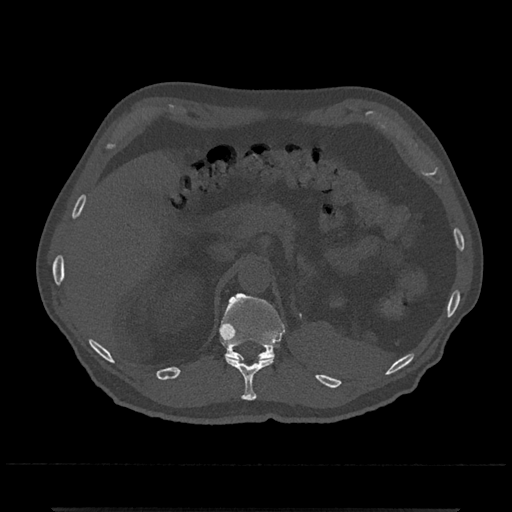
CT including the spine, one axial slice. Slice 459 of 797 in the series (ordered by position). Reconstruction kernel Br40s/3. 120 kVp. Bone window (W 1800 / L 400 HU). 0.5 mm slice thickness. 512 × 512 image matrix. Patient: male, 67 years. From the clinical record (not read from this slice): primary cancer: prostate.
Outlined on this slice (semi-automatic segmentation, software-assisted and operator-edited):
- T11 vertebra: bounding box (x1, y1, x2, y2) in pixels: (225, 356, 274, 401)
- T12 vertebra: (219, 293, 286, 361)